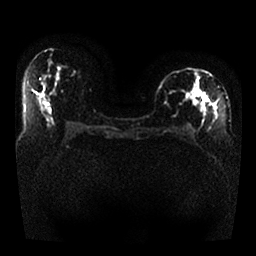
Breast MRI, one axial slice; position 12 of 25 along the scan axis; diffusion-weighted series; image 2 of 4 stored at this slice position (different b-values; order by instance number); 1.5 T; 4 mm slice thickness; 256 × 256 image matrix, field of view 330 × 330 mm. Female patient.
Structures marked on this image (expert manual segmentation):
- tumour on diffusion-weighted imaging: bounding box <182,86,217,115> (left, top, right, bottom; pixels)